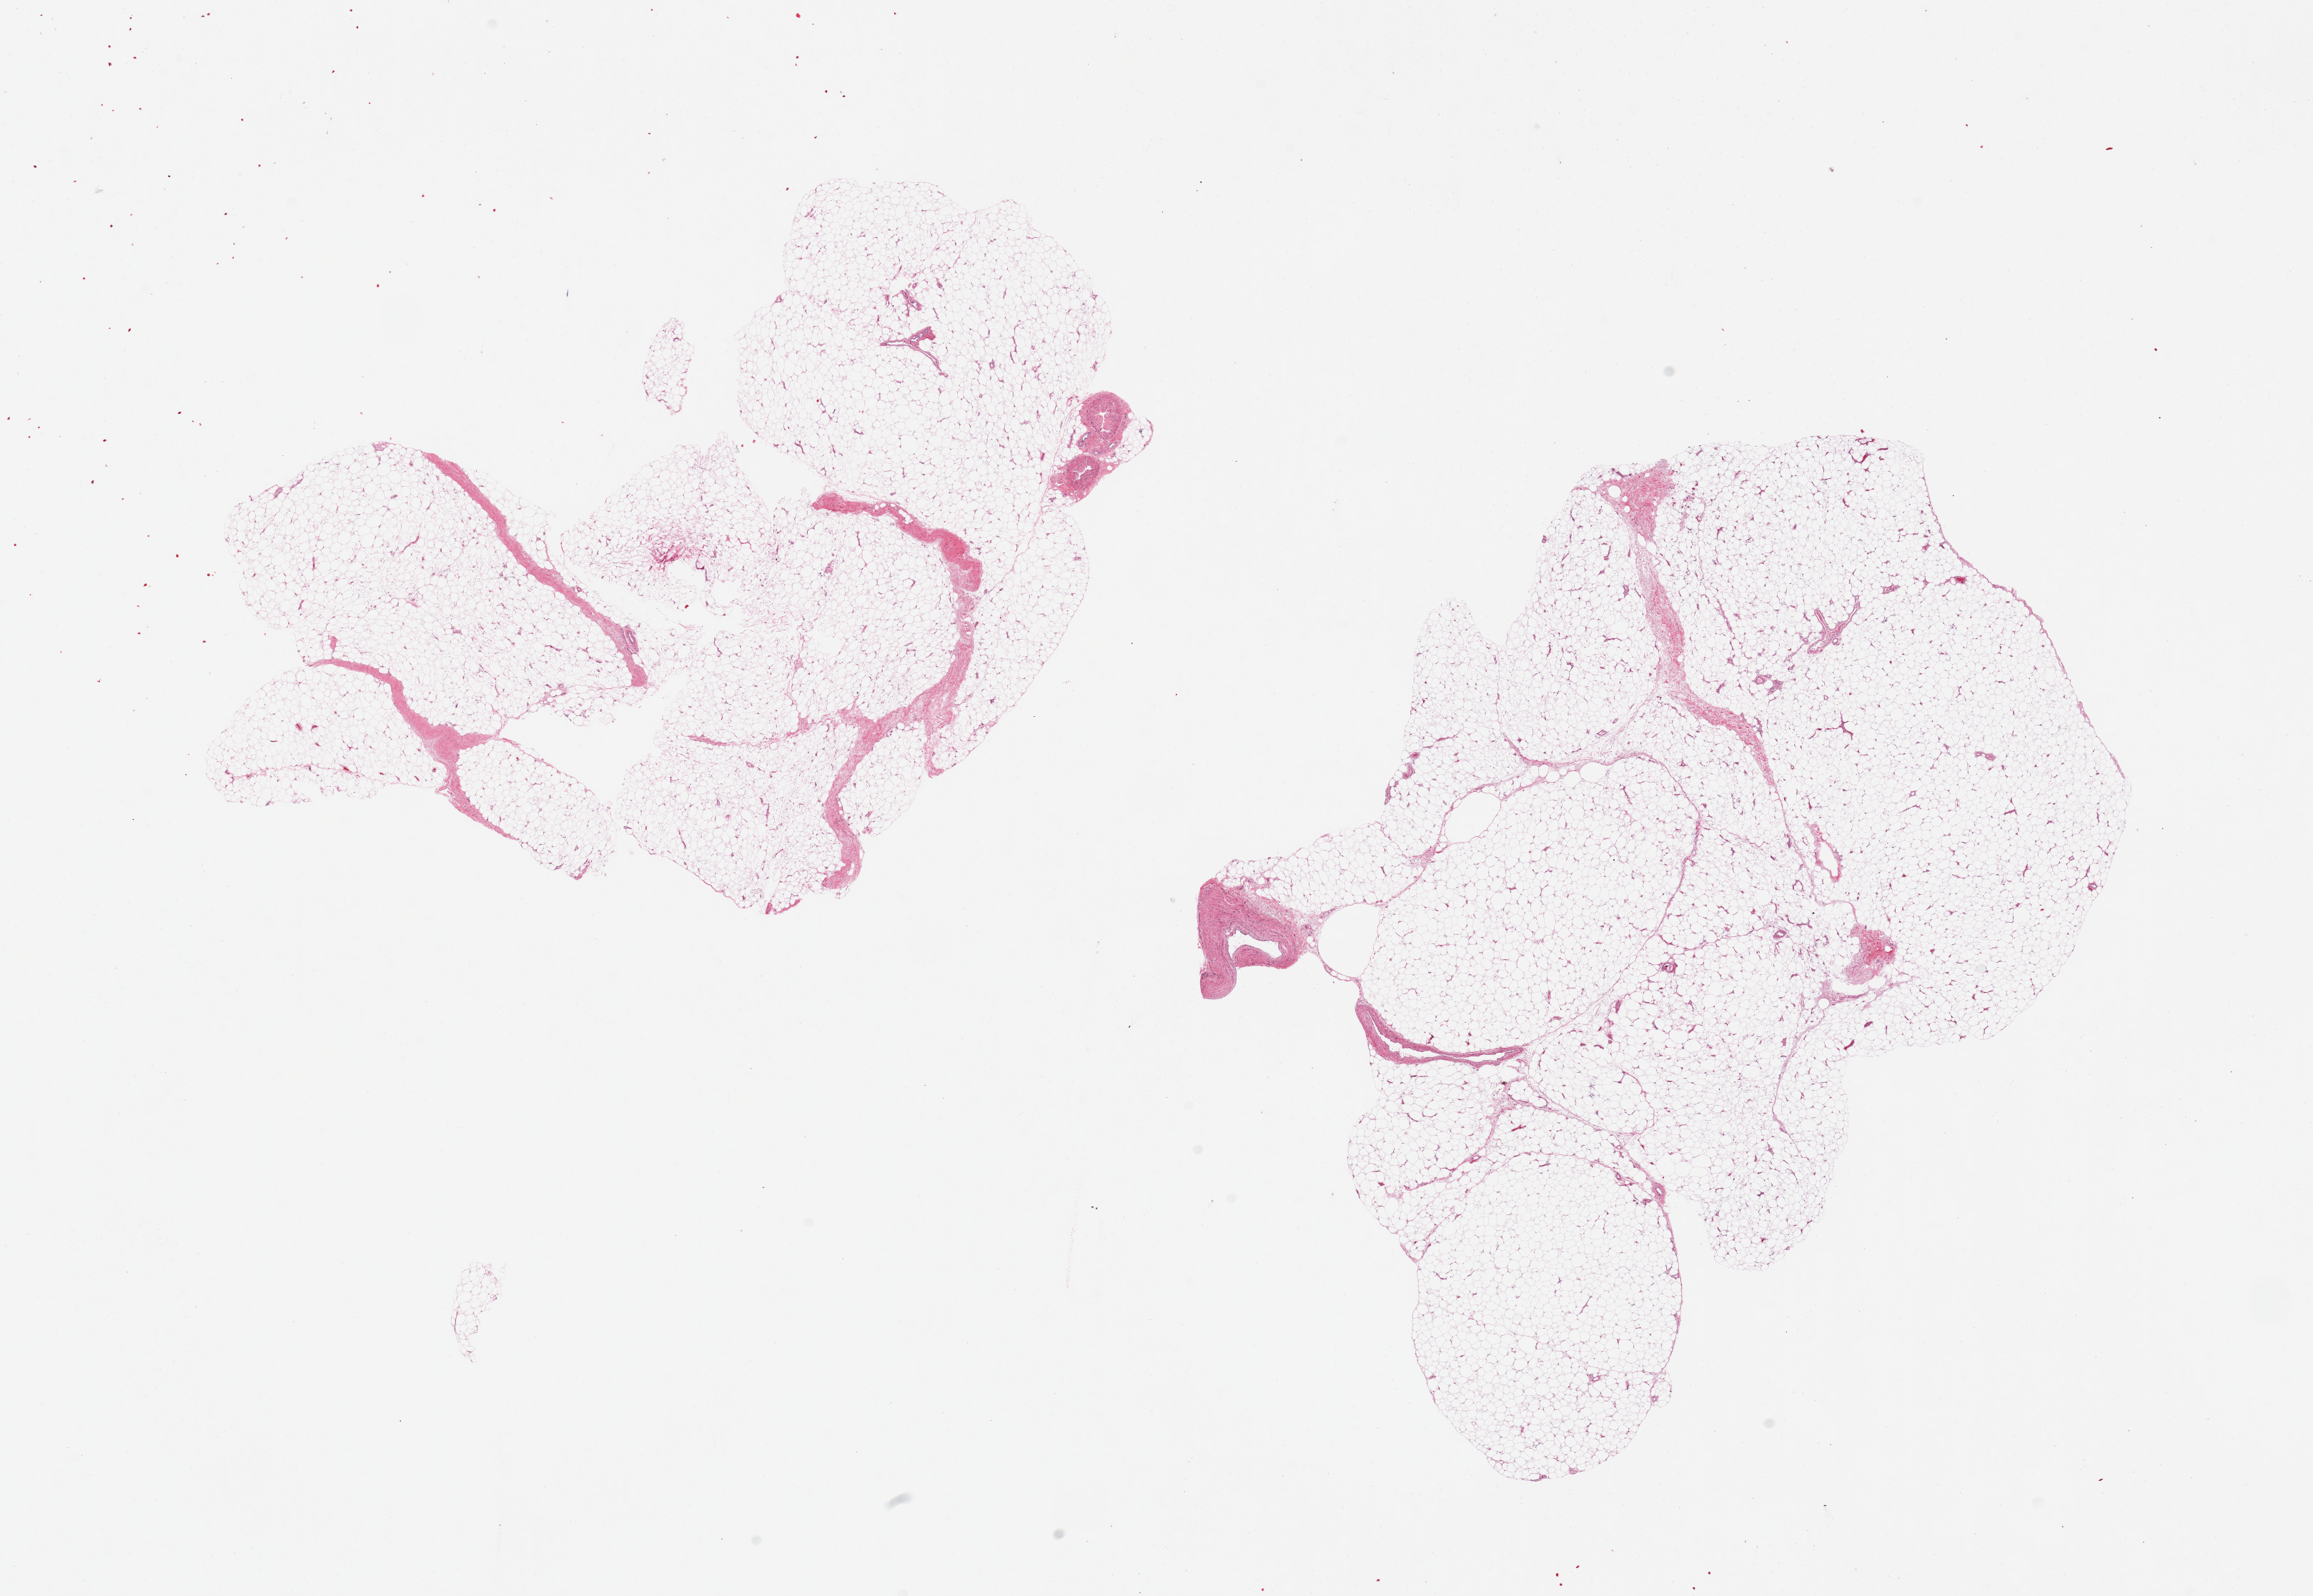
Digitized hematoxylin and eosin (H&E)-stained section — shown as a low-resolution overview of the whole scanned area (about 25.6 x 17.7 mm, acquisition: 20x scan); PAXgene-fixed, paraffin-embedded tissue; target tissue: adipose tissue; donor tissue sample. Female donor.
Review note (as recorded): 2 pieces.